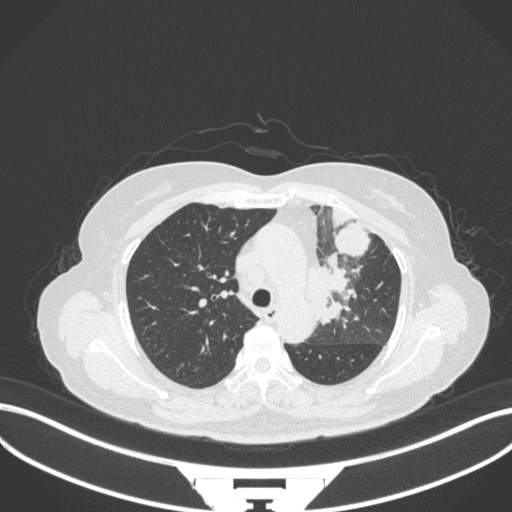
Chest CT, one axial slice. Position 235 of 382 along the scan axis. Reconstruction kernel B31f. 120 kVp. Lung window (W 1500 / L -600 HU). 512 × 512 image matrix, field of view 400 × 400 mm. Patient: female, 64 years. From the clinical record (not read from this slice): clinical TNM (as recorded): T2a N2 M0.
Outlined on this slice (rectangle marked by the reading radiologist):
- lung tumour (recorded histology: adenocarcinoma): box from (x=308, y=248) to (x=358, y=327) px
- lung tumour (recorded histology: adenocarcinoma): (x=333, y=219)–(x=376, y=258)